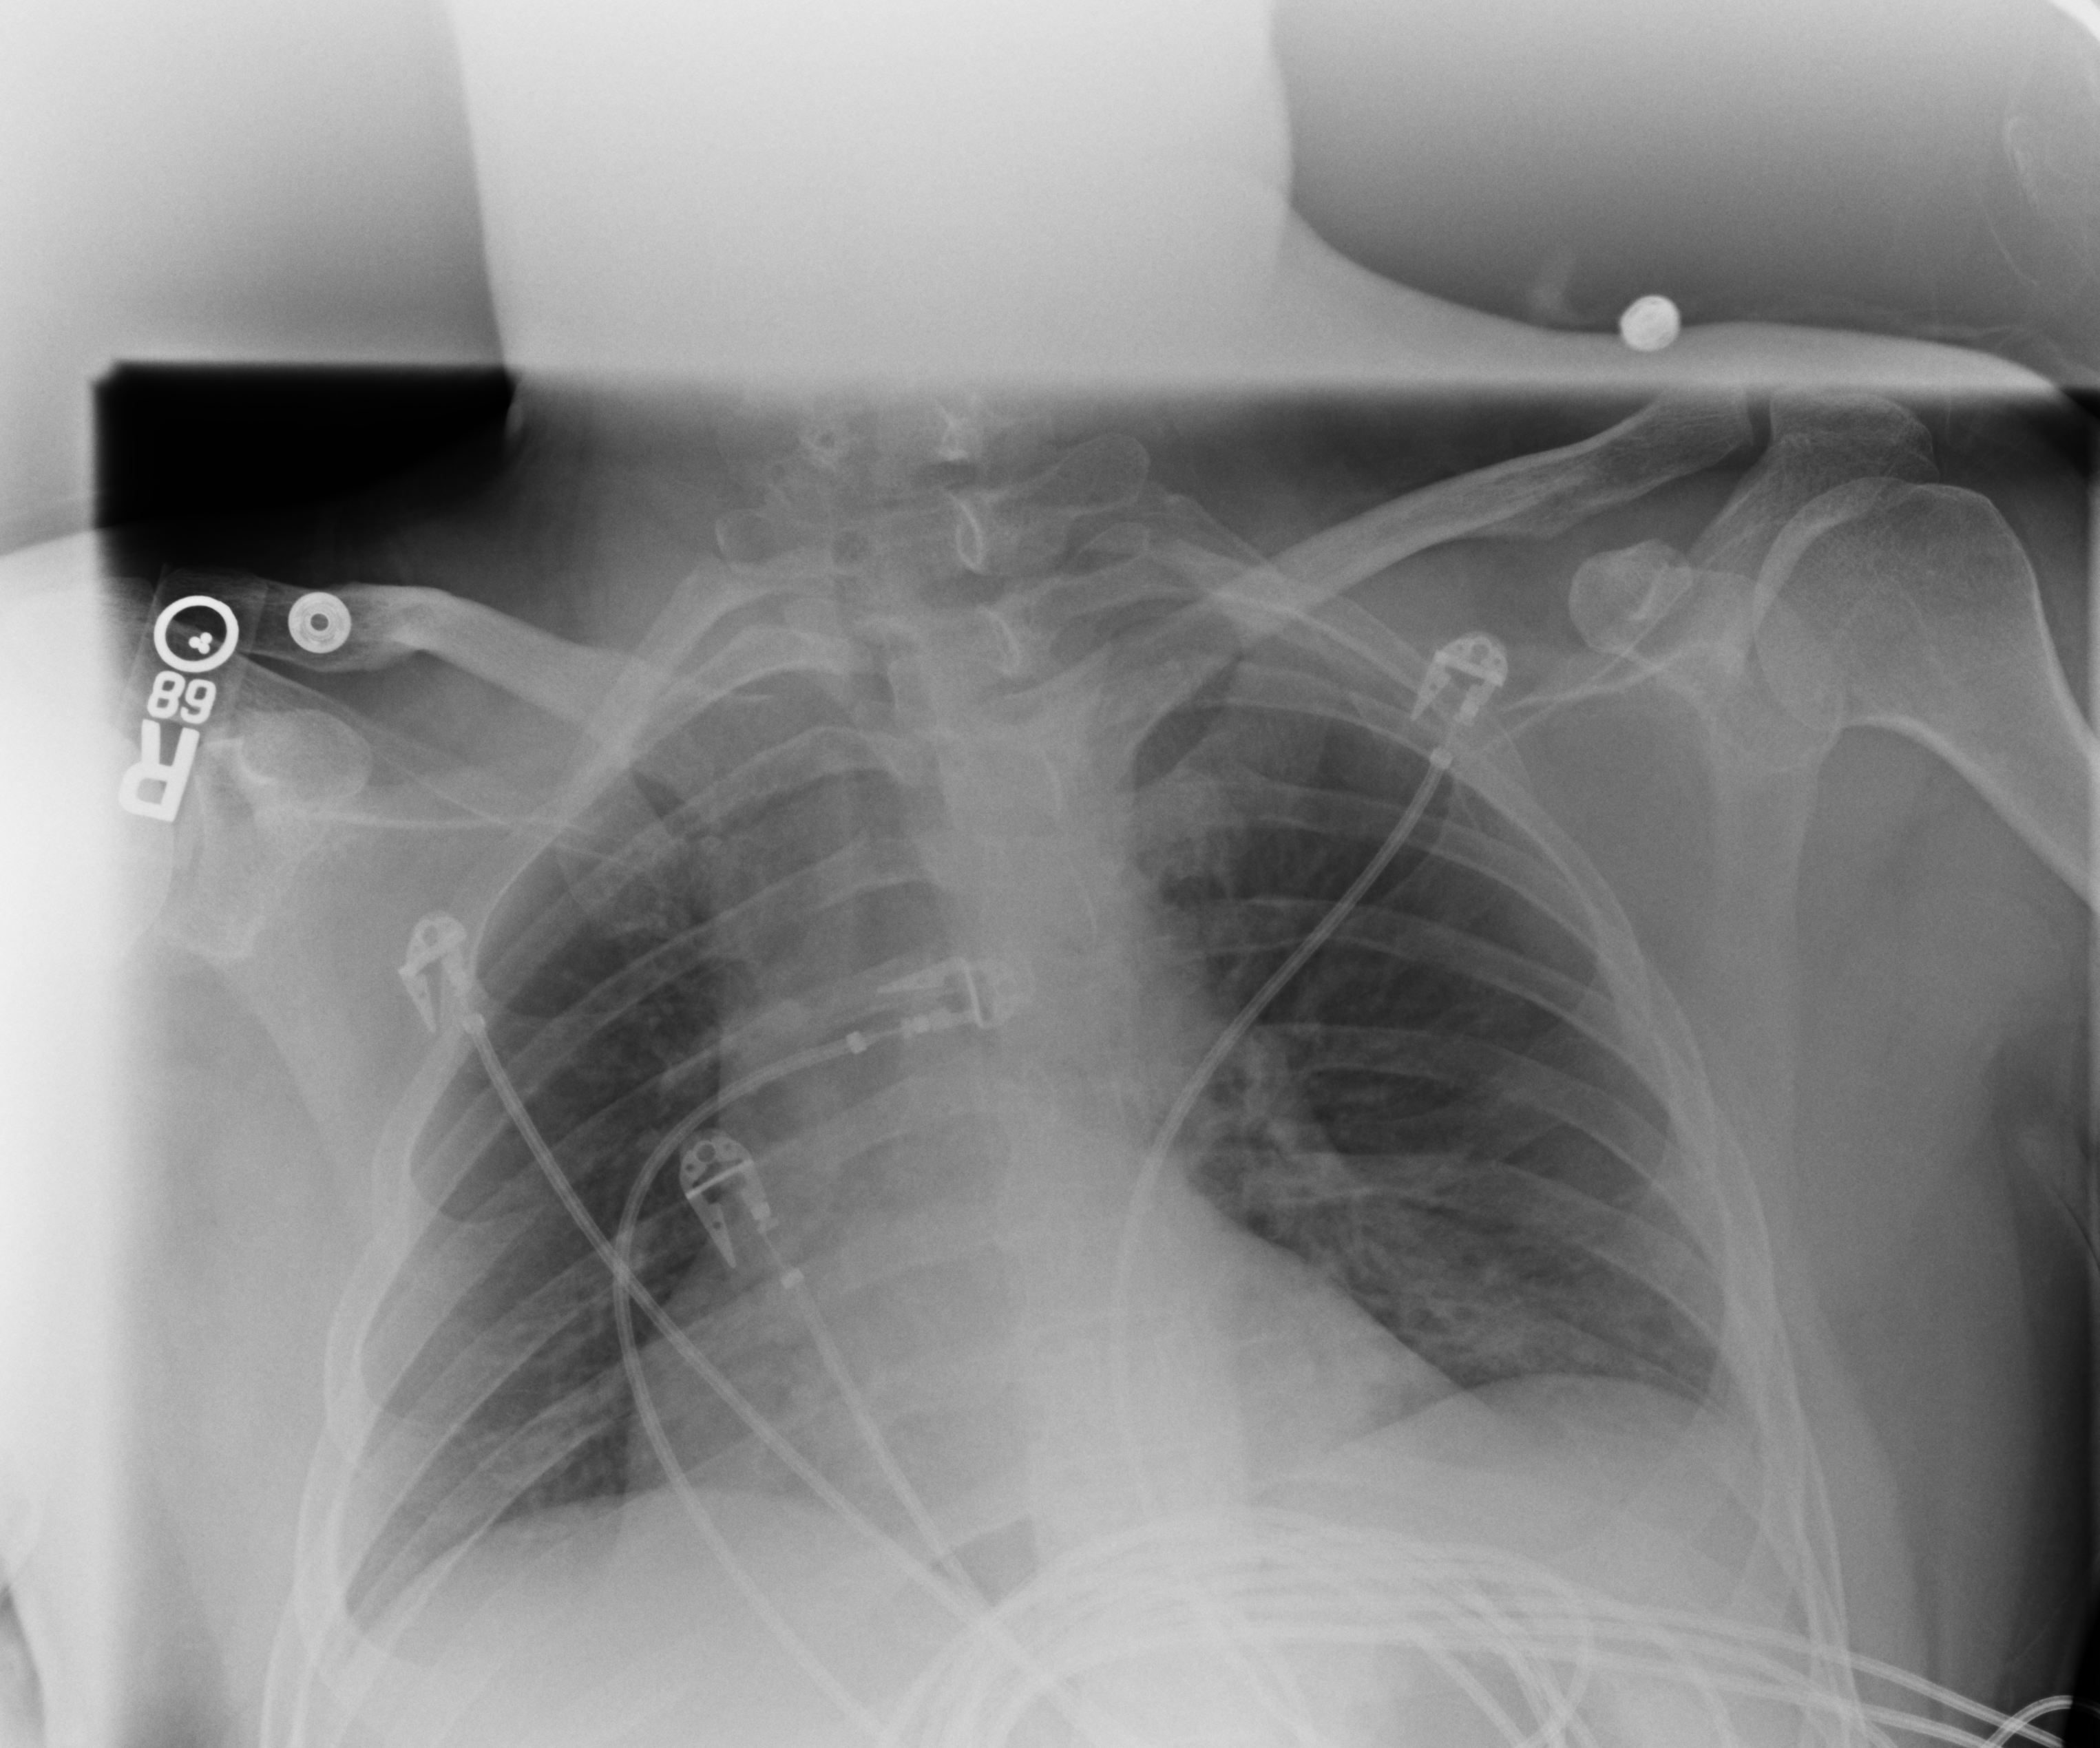
Bedside chest radiograph (computed radiography); anteroposterior (AP) projection. Male patient hospitalised with COVID-19, age 18–59 years.
Hospital-stay facts (about this admission, not read from this image; timing relative to this image not recorded): admitted to intensive care during this hospital stay: yes; mechanically ventilated during this hospital stay: yes.